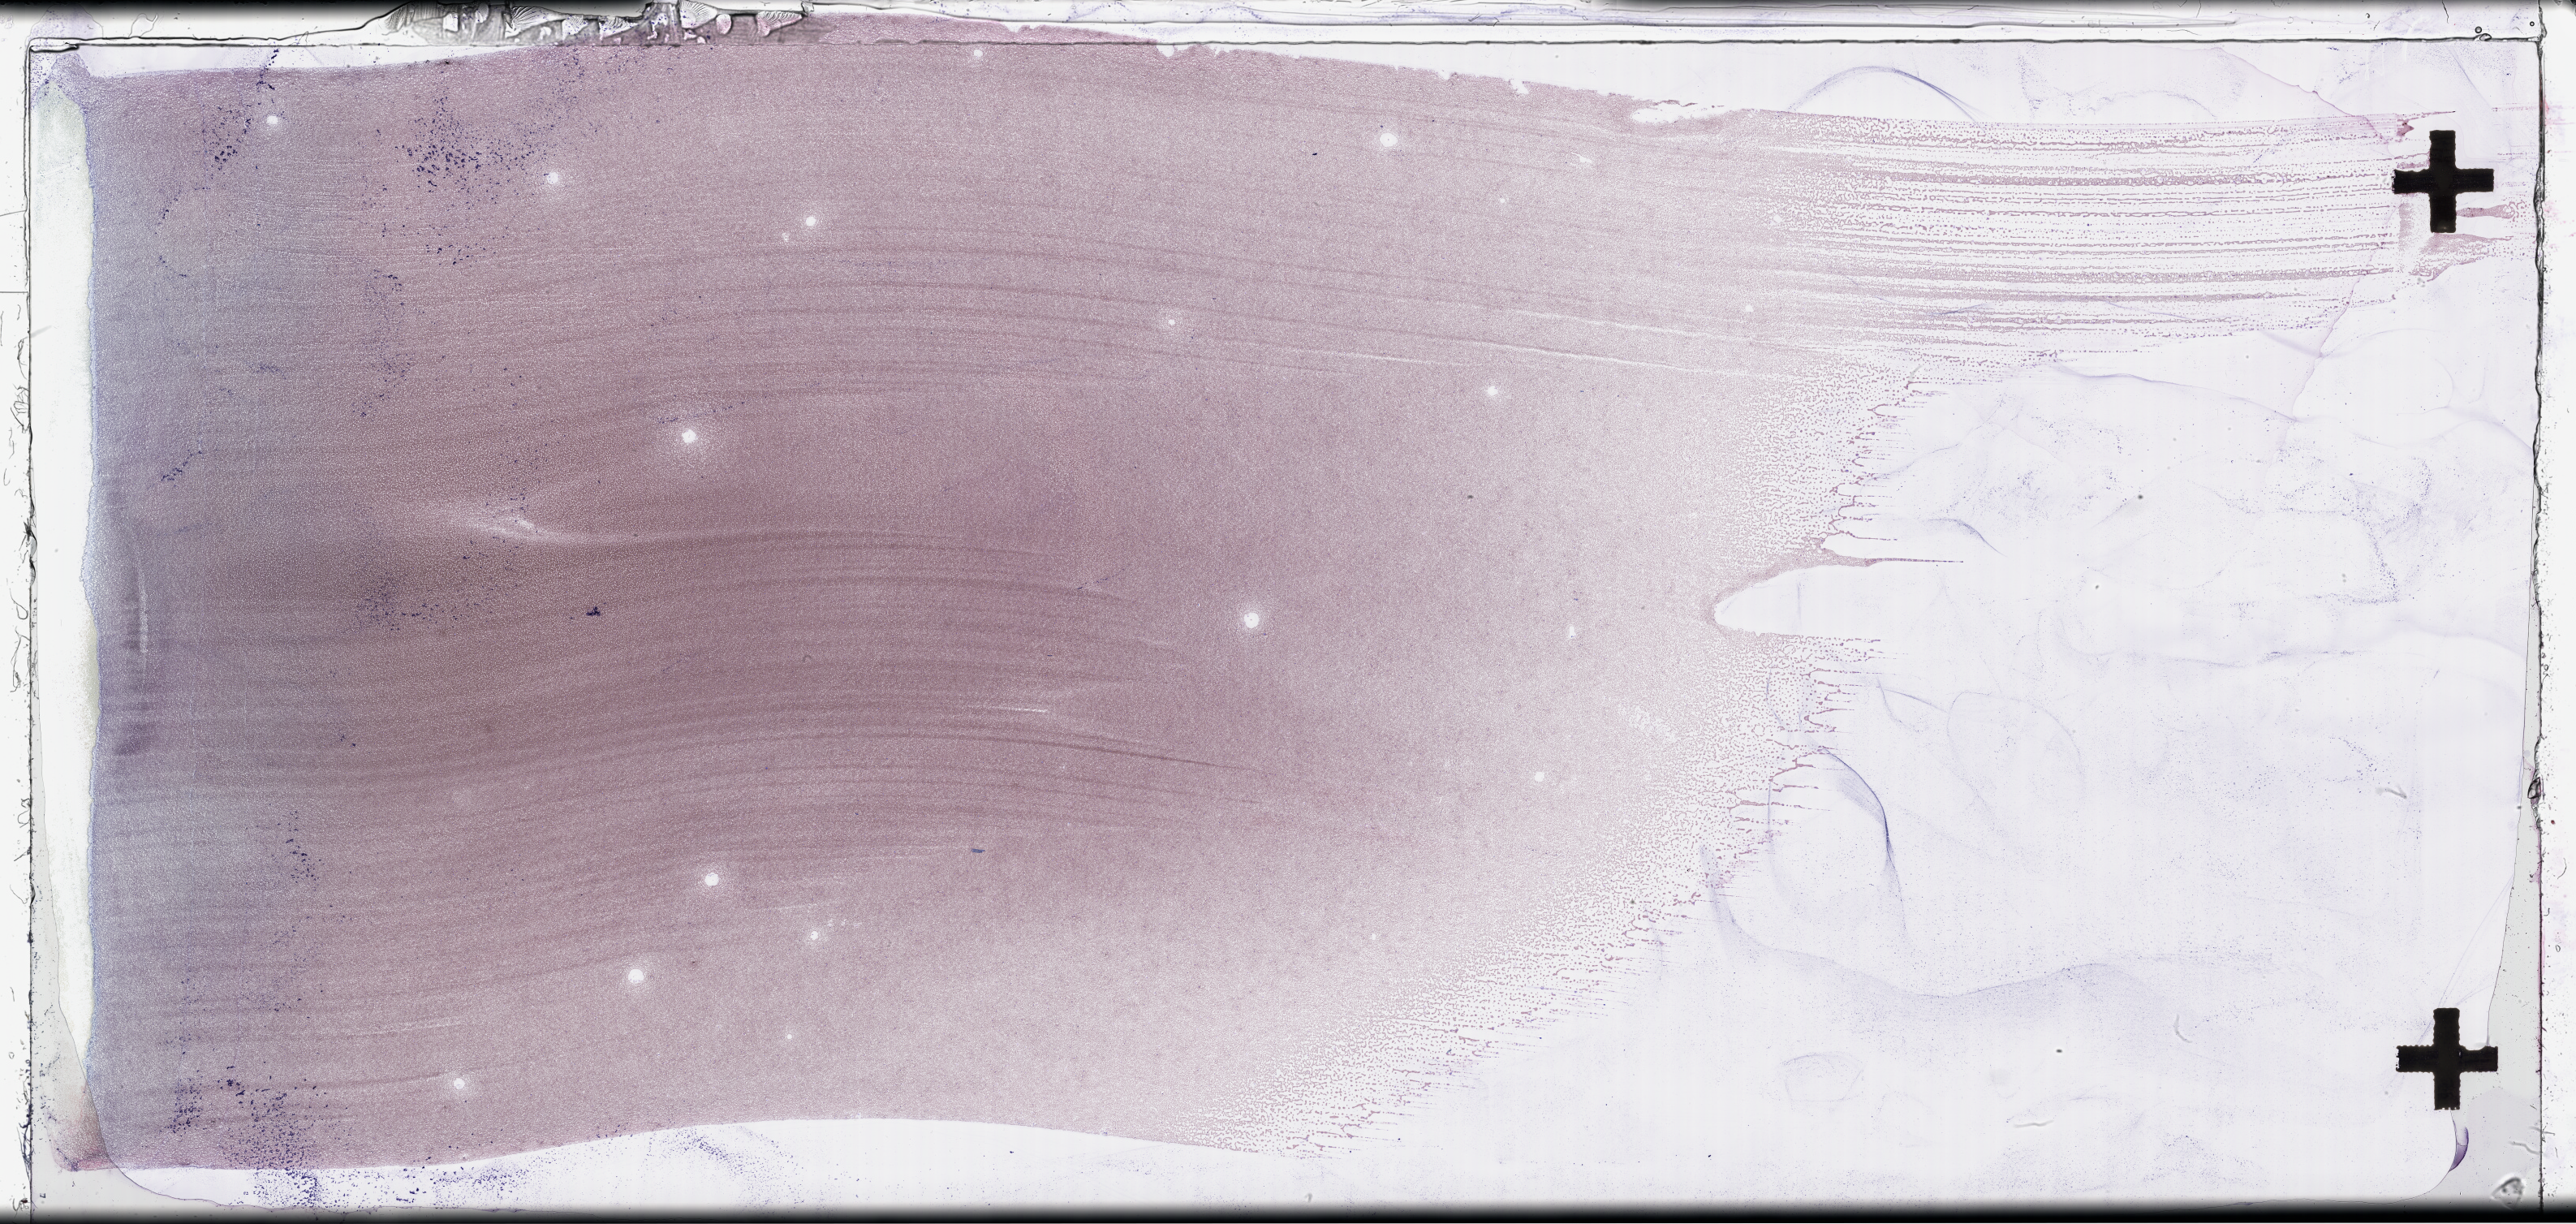
Wright–Giemsa-stained bone marrow smear, whole-slide image — shown as a low-resolution overview of the whole scanned area (about 51.3 x 24.4 mm), smear from an EDTA sample. Patient: female.
Patient diagnosis: Plasma Cell Myeloma.